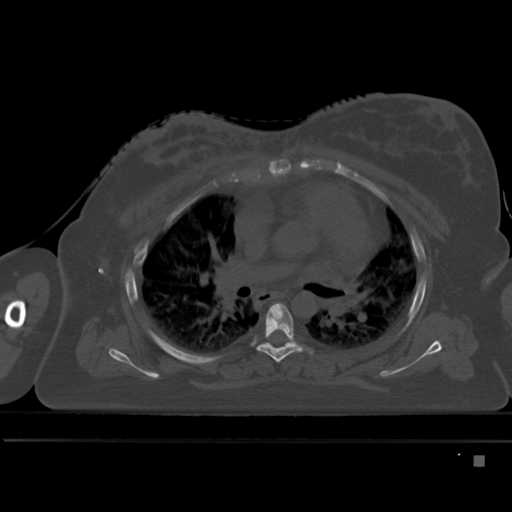
CT including the spine, one axial slice; position 319 of 495 along the scan axis; bone window (W 1800 / L 400 HU); 1.5 mm slice thickness; 512 × 512 image matrix. Female patient, age 33 years. From the clinical record (not read from this slice): primary cancer: breast; vertebrae with lytic lesions (as recorded): T1.
Structures marked on this image (semi-automatically segmented with operator editing):
- T5 vertebra: bounding box <257,303,303,363> (left, top, right, bottom; pixels)
- T6 vertebra: <261,343,270,345>